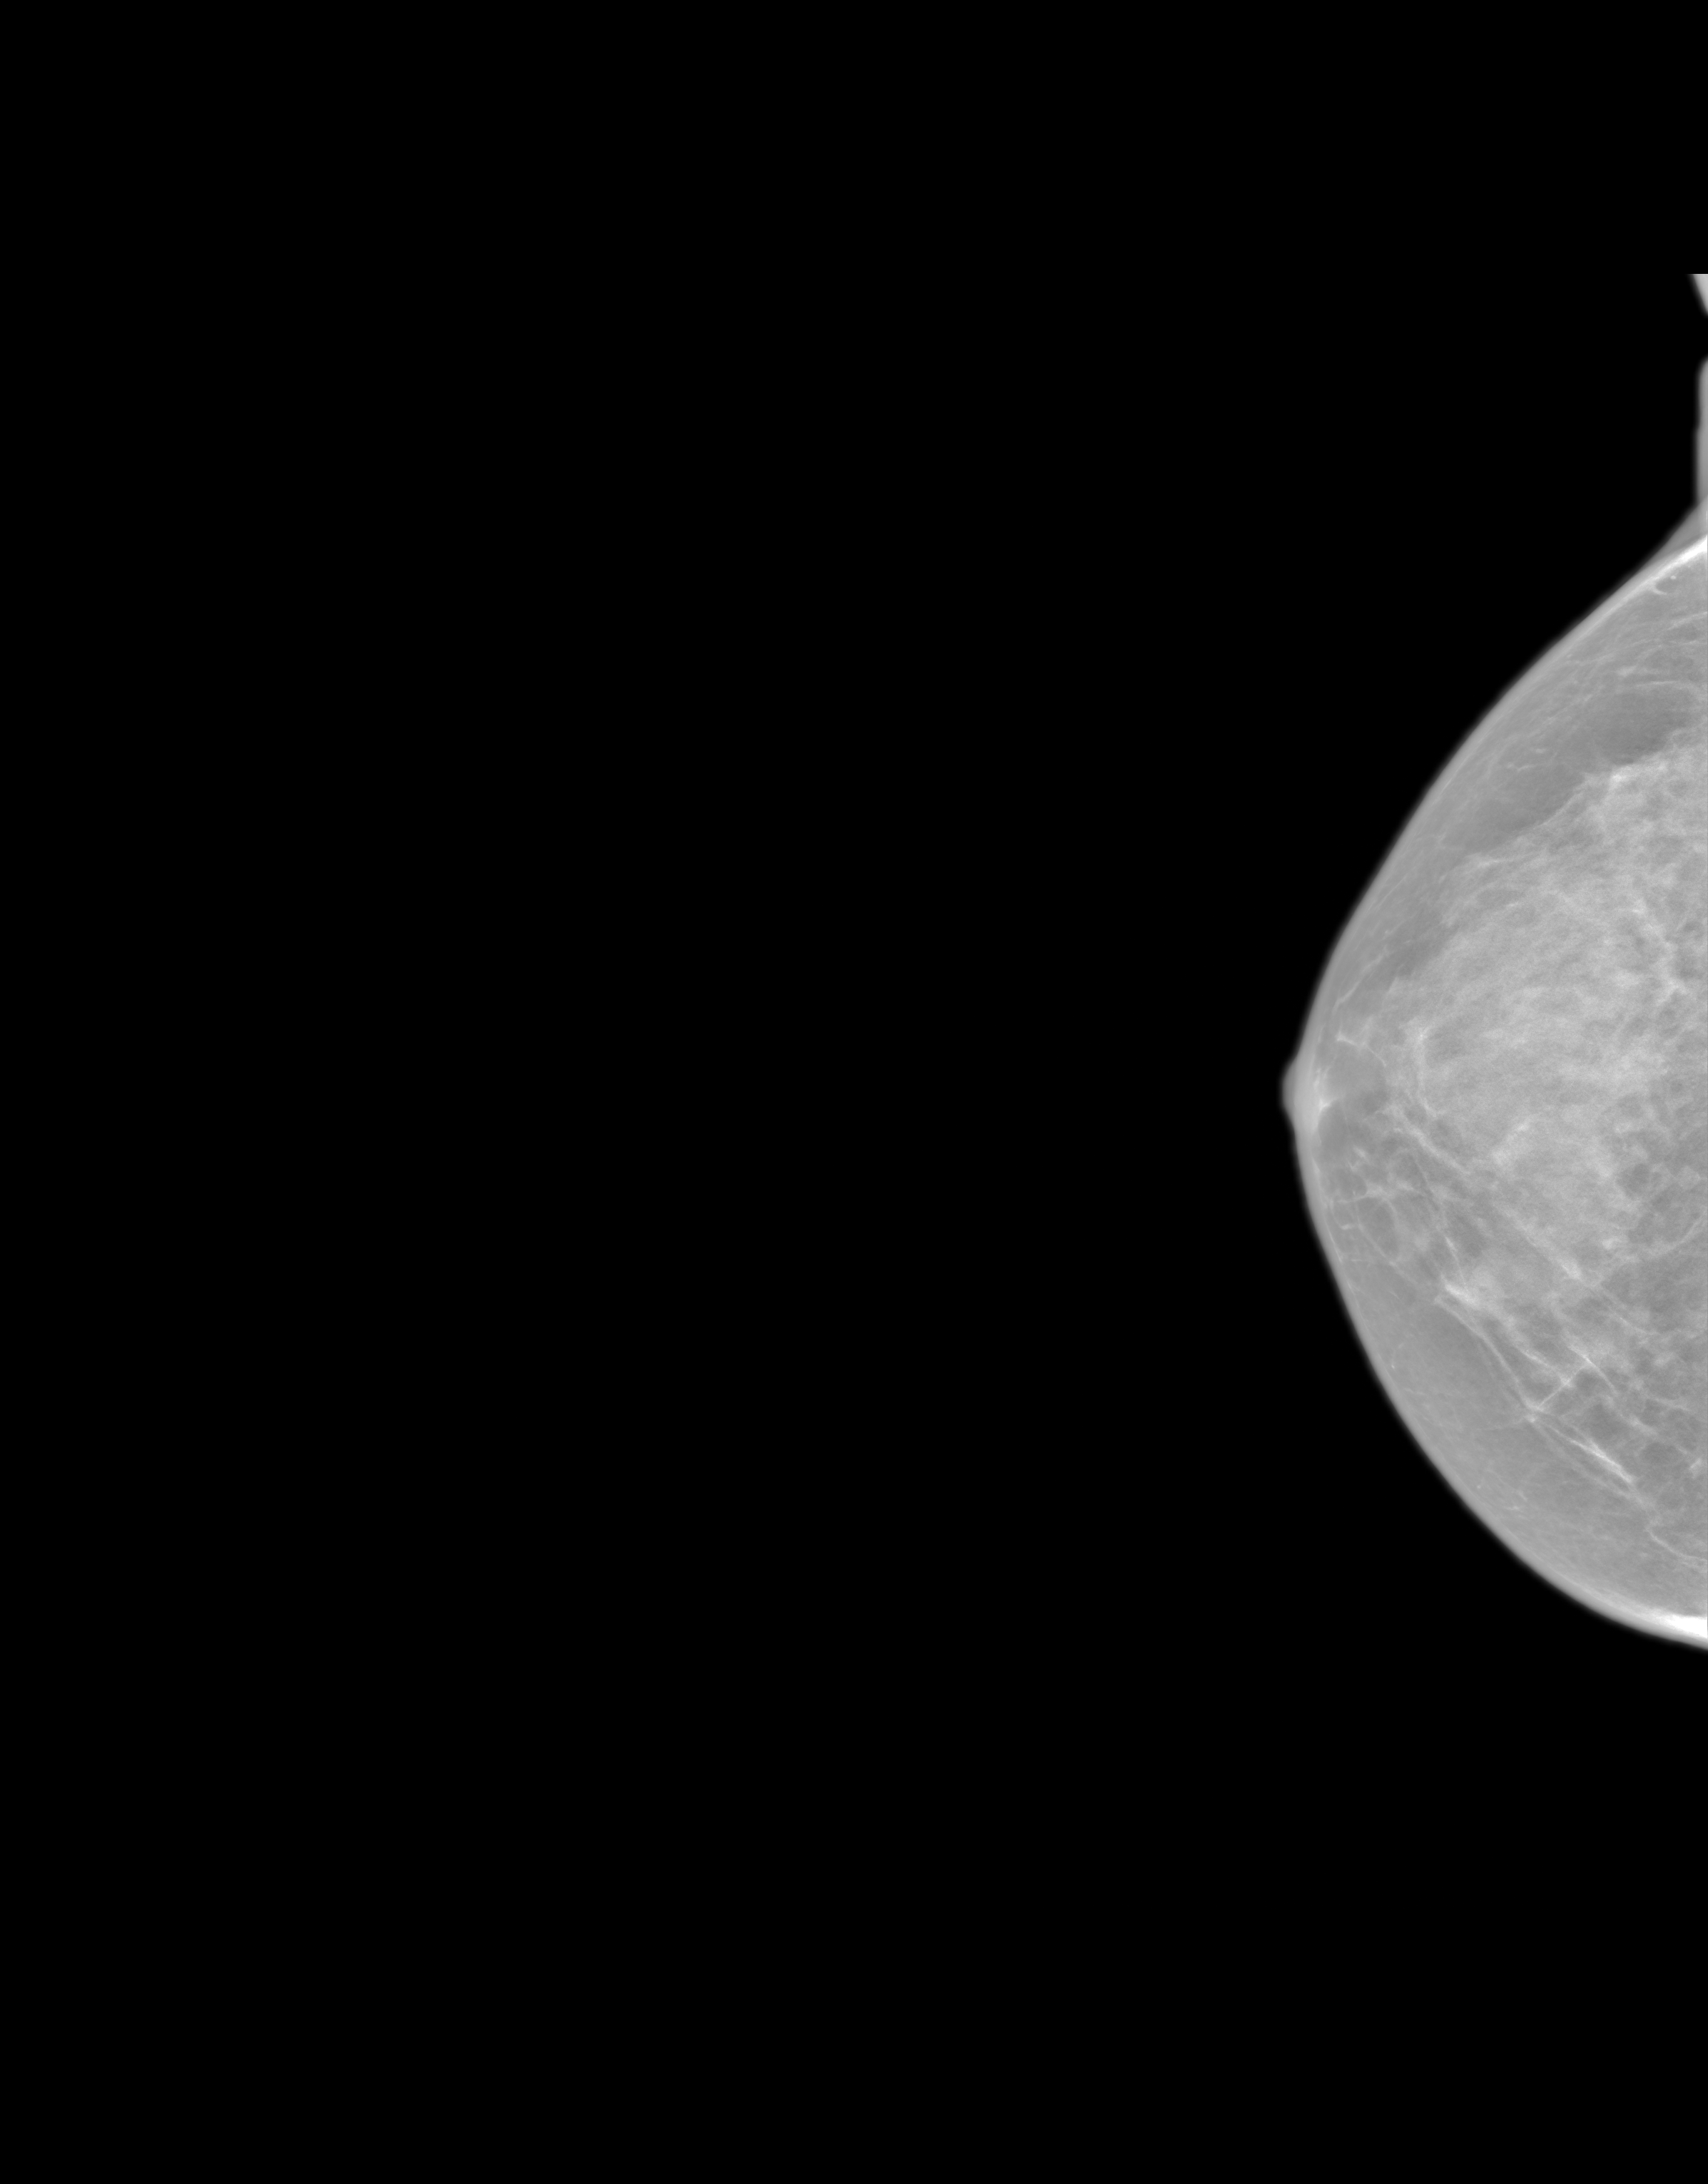
Screening examination. Patient: female, 56 years.
Image type: synthesized 2-D view from tomosynthesis. Breast: right. Projection: cranio-caudal projection.